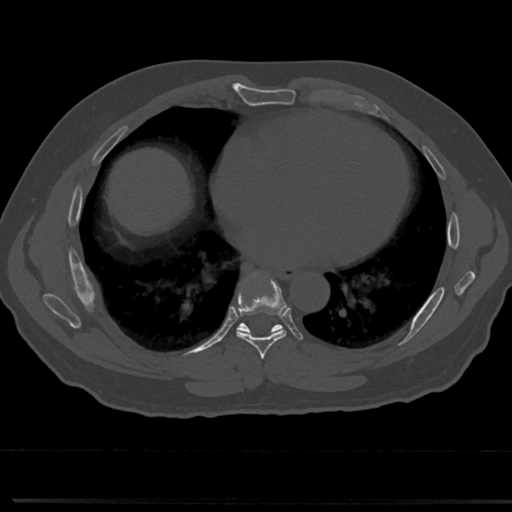
CT including the spine, one axial slice; position 389 of 817 along the scan axis; reconstruction kernel Br40s/3; bone window (W 1800 / L 400 HU); 0.5 mm slice thickness; 512 × 512 image matrix, field of view 355 × 355 mm. Patient: male, 61 years. Case-level facts recorded for this patient, not image findings: primary cancer: prostate.
Annotated regions visible in this slice (semi-automatic segmentation, software-assisted and operator-edited):
- T6 vertebra: bounding box <260,360,269,377> (left, top, right, bottom; pixels)
- T7 vertebra: <215,275,310,356>